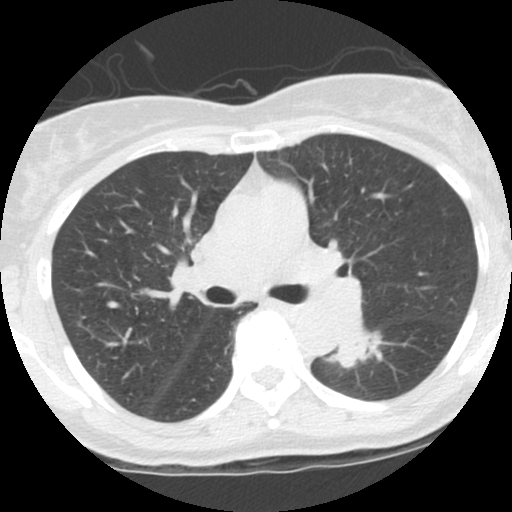
Low-dose screening chest CT, one axial slice; slice 68 of 115 in the series (ordered by position); reconstruction kernel STANDARD; lung window (W 1500 / L -600 HU); 2.5 mm slice thickness; 512 × 512 image matrix, field of view 290 × 290 mm.
Annotated regions visible in this slice (manually delineated by an expert):
- lesion 1 (tumor, lower lobe of left lung): box from (x=329, y=326) to (x=382, y=368) px